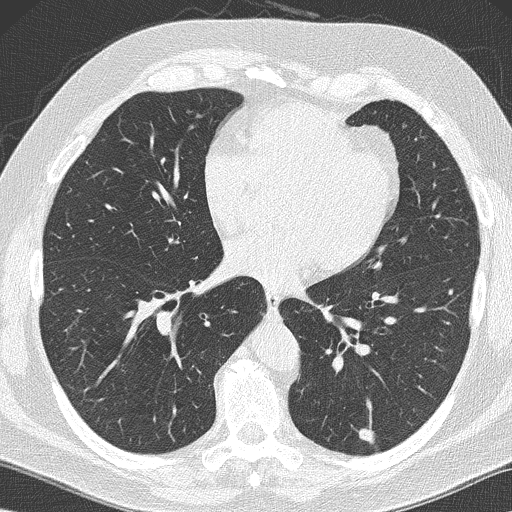
Axial slice from a low-dose chest CT screening exam. Baseline screening round. Lung window (W 1500 / L -600 HU). 2 mm slice thickness. 120 kVp. Slice 94 of 152 in the series. 512 × 512 image matrix, field of view 350 × 350 mm. Male participant, aged 59 years at enrolment. Former smoker at enrolment.
Expert-annotated lung lesion, bounding box <345,417,386,453> (left, top, right, bottom; pixels). The screening reader recorded 2 non-calcified nodules or masses ≥4 mm on this exam (left lower lobe, left lower lobe); which of them this box marks is not recorded. Official screen result: positive, change unspecified: nodule(s) >= 4 mm or enlarging nodule(s), mass(es), or other non-specific abnormalities suspicious for lung cancer. Later outcome: lung cancer diagnosed 61 days after this screen — large cell carcinoma, NOS, left lower lobe, poorly differentiated (G3), stage IA (AJCC 6th edition), 14 mm at pathology.